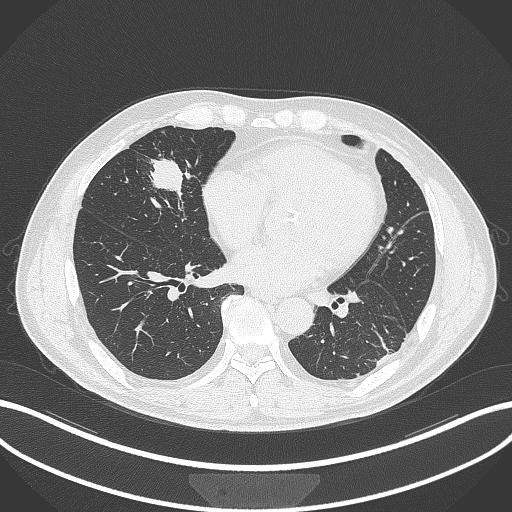
Chest CT, one axial slice; slice 112 of 399 in the series (ordered by position); reconstruction kernel B70f; lung window (W 1500 / L -600 HU); 1 mm slice thickness; 512 × 512 image matrix, field of view 400 × 400 mm. Male patient, age 59 years. From the clinical record (not read from this slice): clinical TNM (as recorded): T2a N1 M0.
Outlined on this slice (rectangle marked by the reading radiologist):
- lung tumour (recorded histology: adenocarcinoma): bounding box (x1, y1, x2, y2) in pixels: (142, 153, 193, 194)